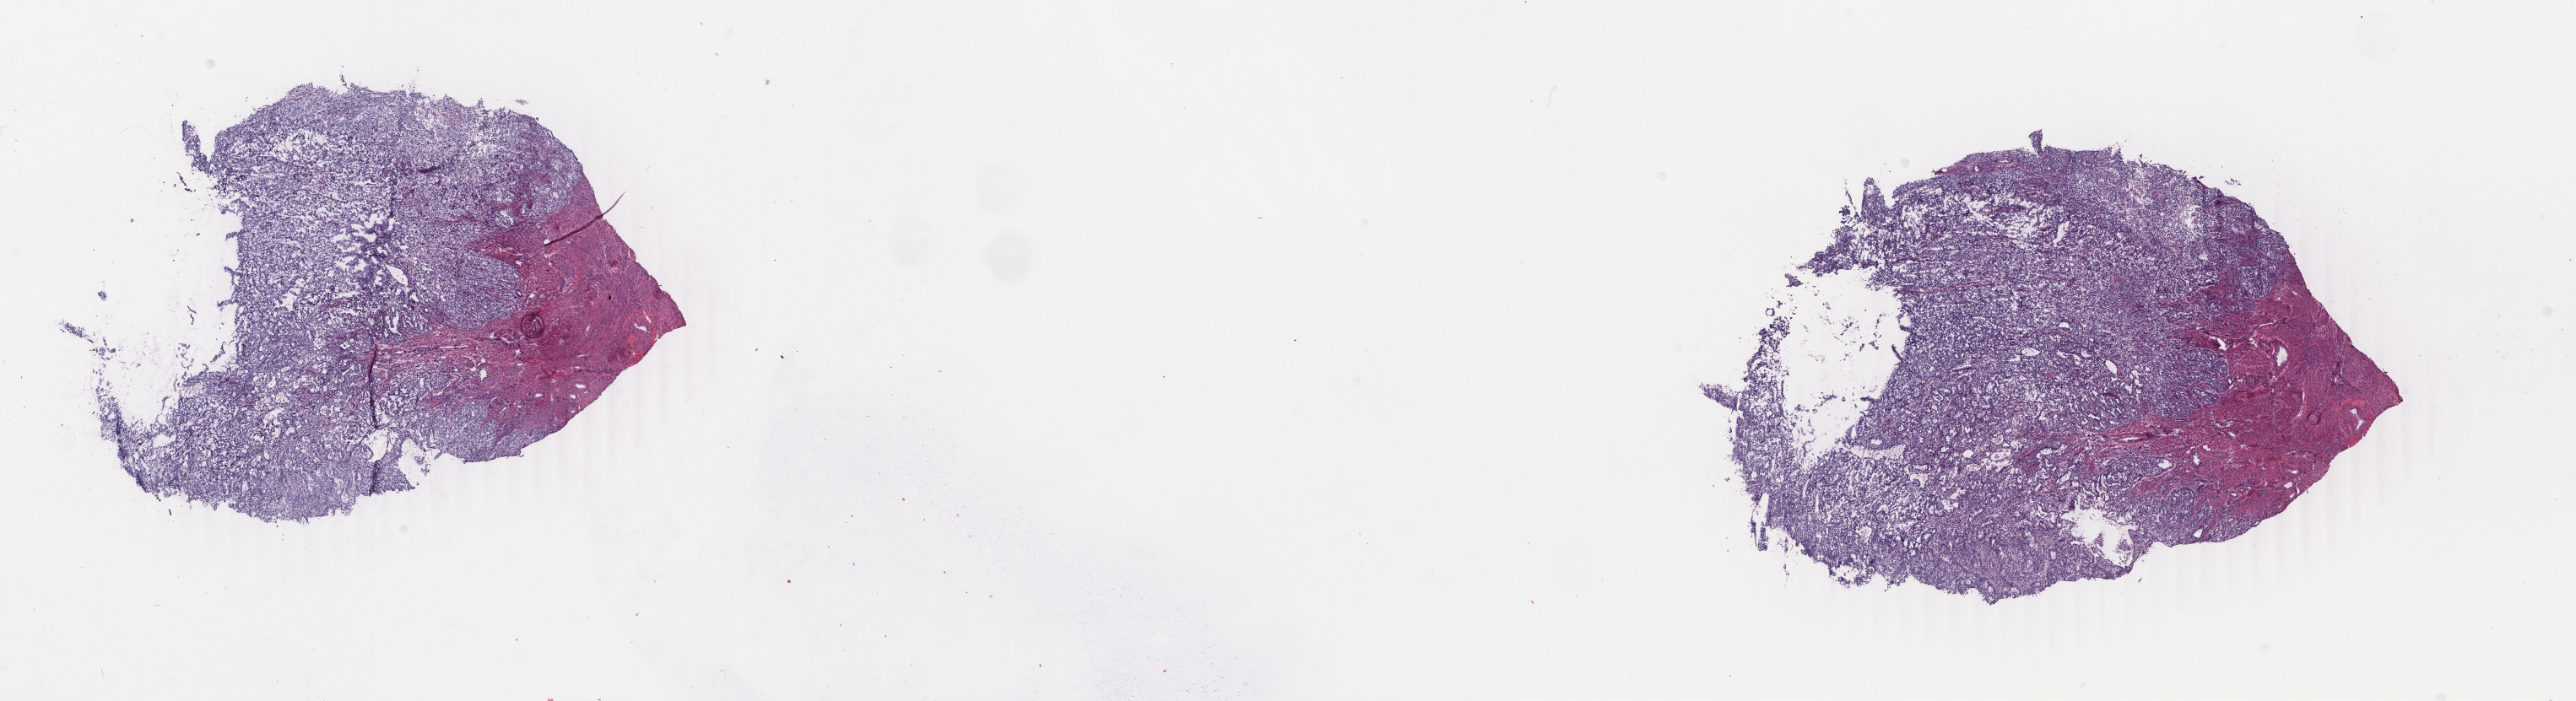
Digitized H&E-stained tissue section (whole slide), shown as a low-resolution overview of the whole scanned area (about 24.3 x 6.6 mm, from a 40x scan). Frozen section. Sample: primary tumour, uterus. Patient: female, age at initial diagnosis 53 years.
Pathologic diagnosis: Endometrioid adenocarcinoma, NOS (endometrium).